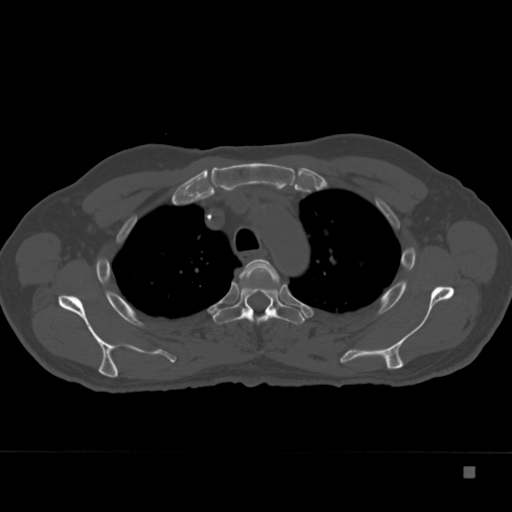
CT including the spine, one axial slice. Position 276 of 332 along the scan axis. Bone window (W 1800 / L 400 HU). 512 × 512 image matrix, field of view 389 × 389 mm. Patient: male, 72 years. Case-level facts recorded for this patient, not image findings: primary cancer: skeletal.
Structures marked on this image (semi-automatically segmented with operator editing):
- T3 vertebra: bounding box <238,259,280,300> (left, top, right, bottom; pixels)
- T4 vertebra: <213,277,305,325>